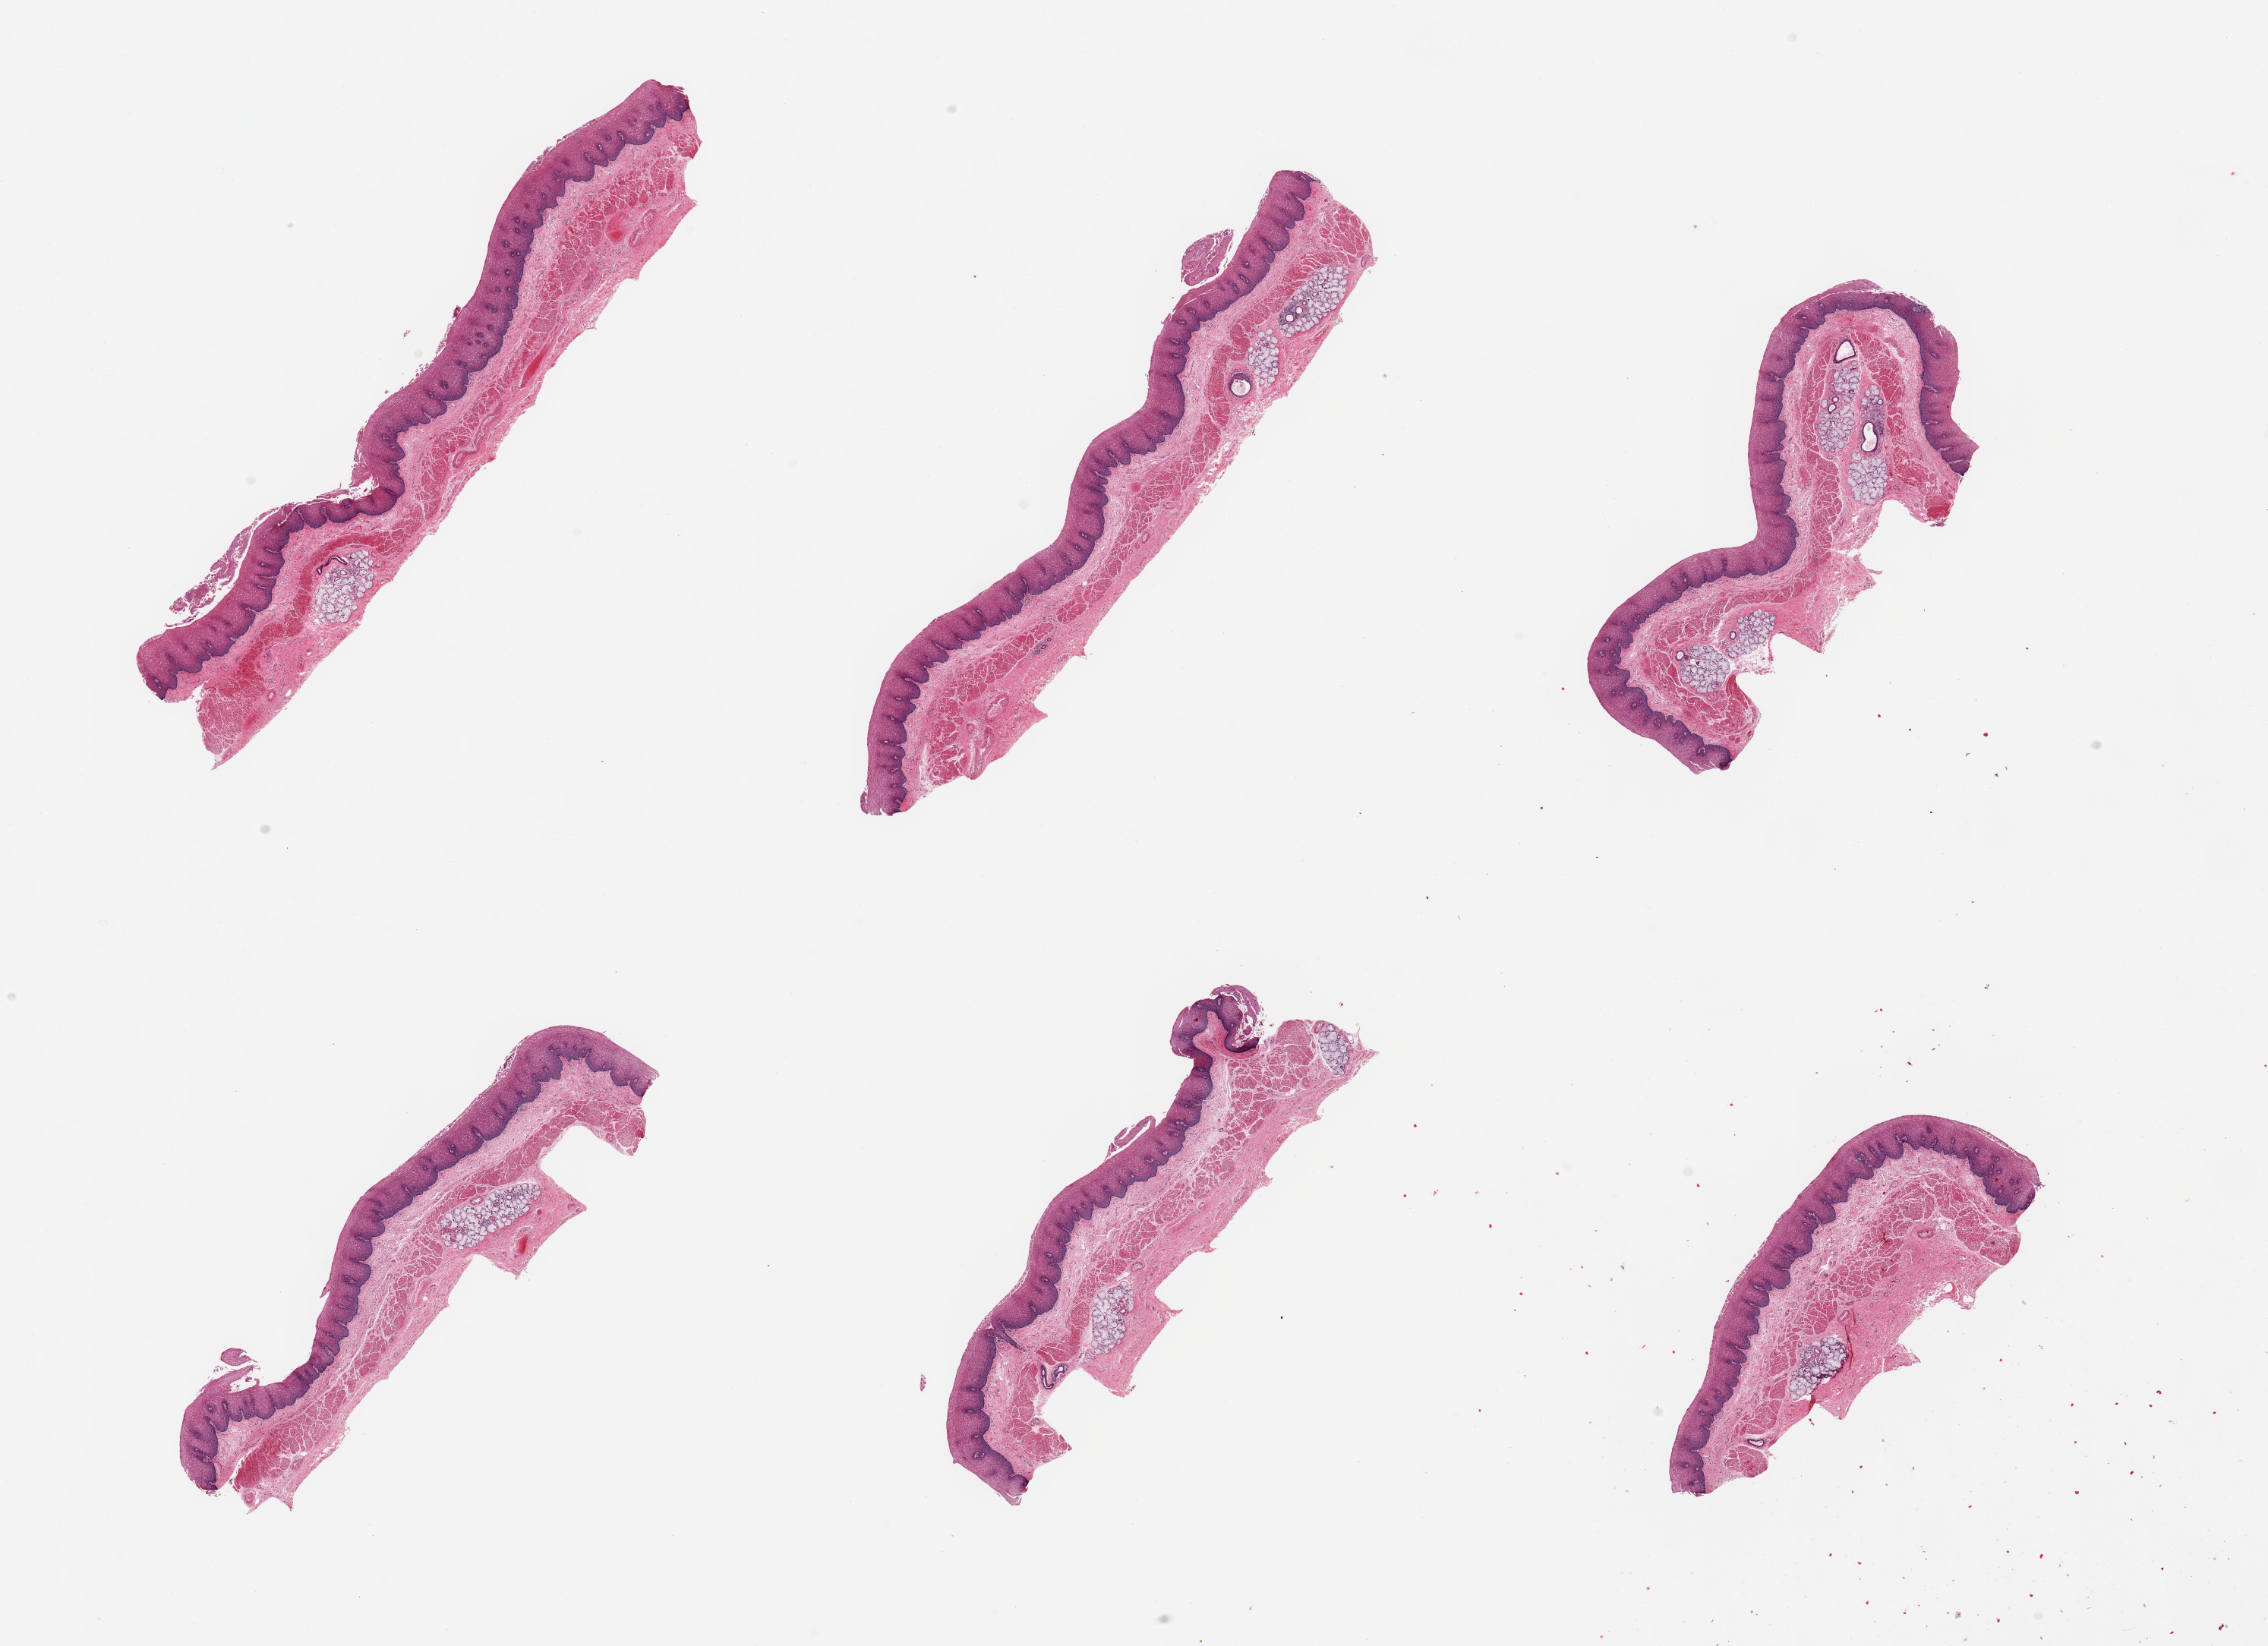
Whole-slide image, haematoxylin and eosin stain, brightfield — a low-resolution overview of the entire scanned area, about 23.6 x 17.1 mm. PAXgene-fixed paraffin-embedded (PFPE) section. Target tissue: esophageal mucous membrane. Donor tissue sample. Female donor.
Review note (as recorded): 6 pieces; well preserved; submucosal glands occupy 5-10% in each piece.